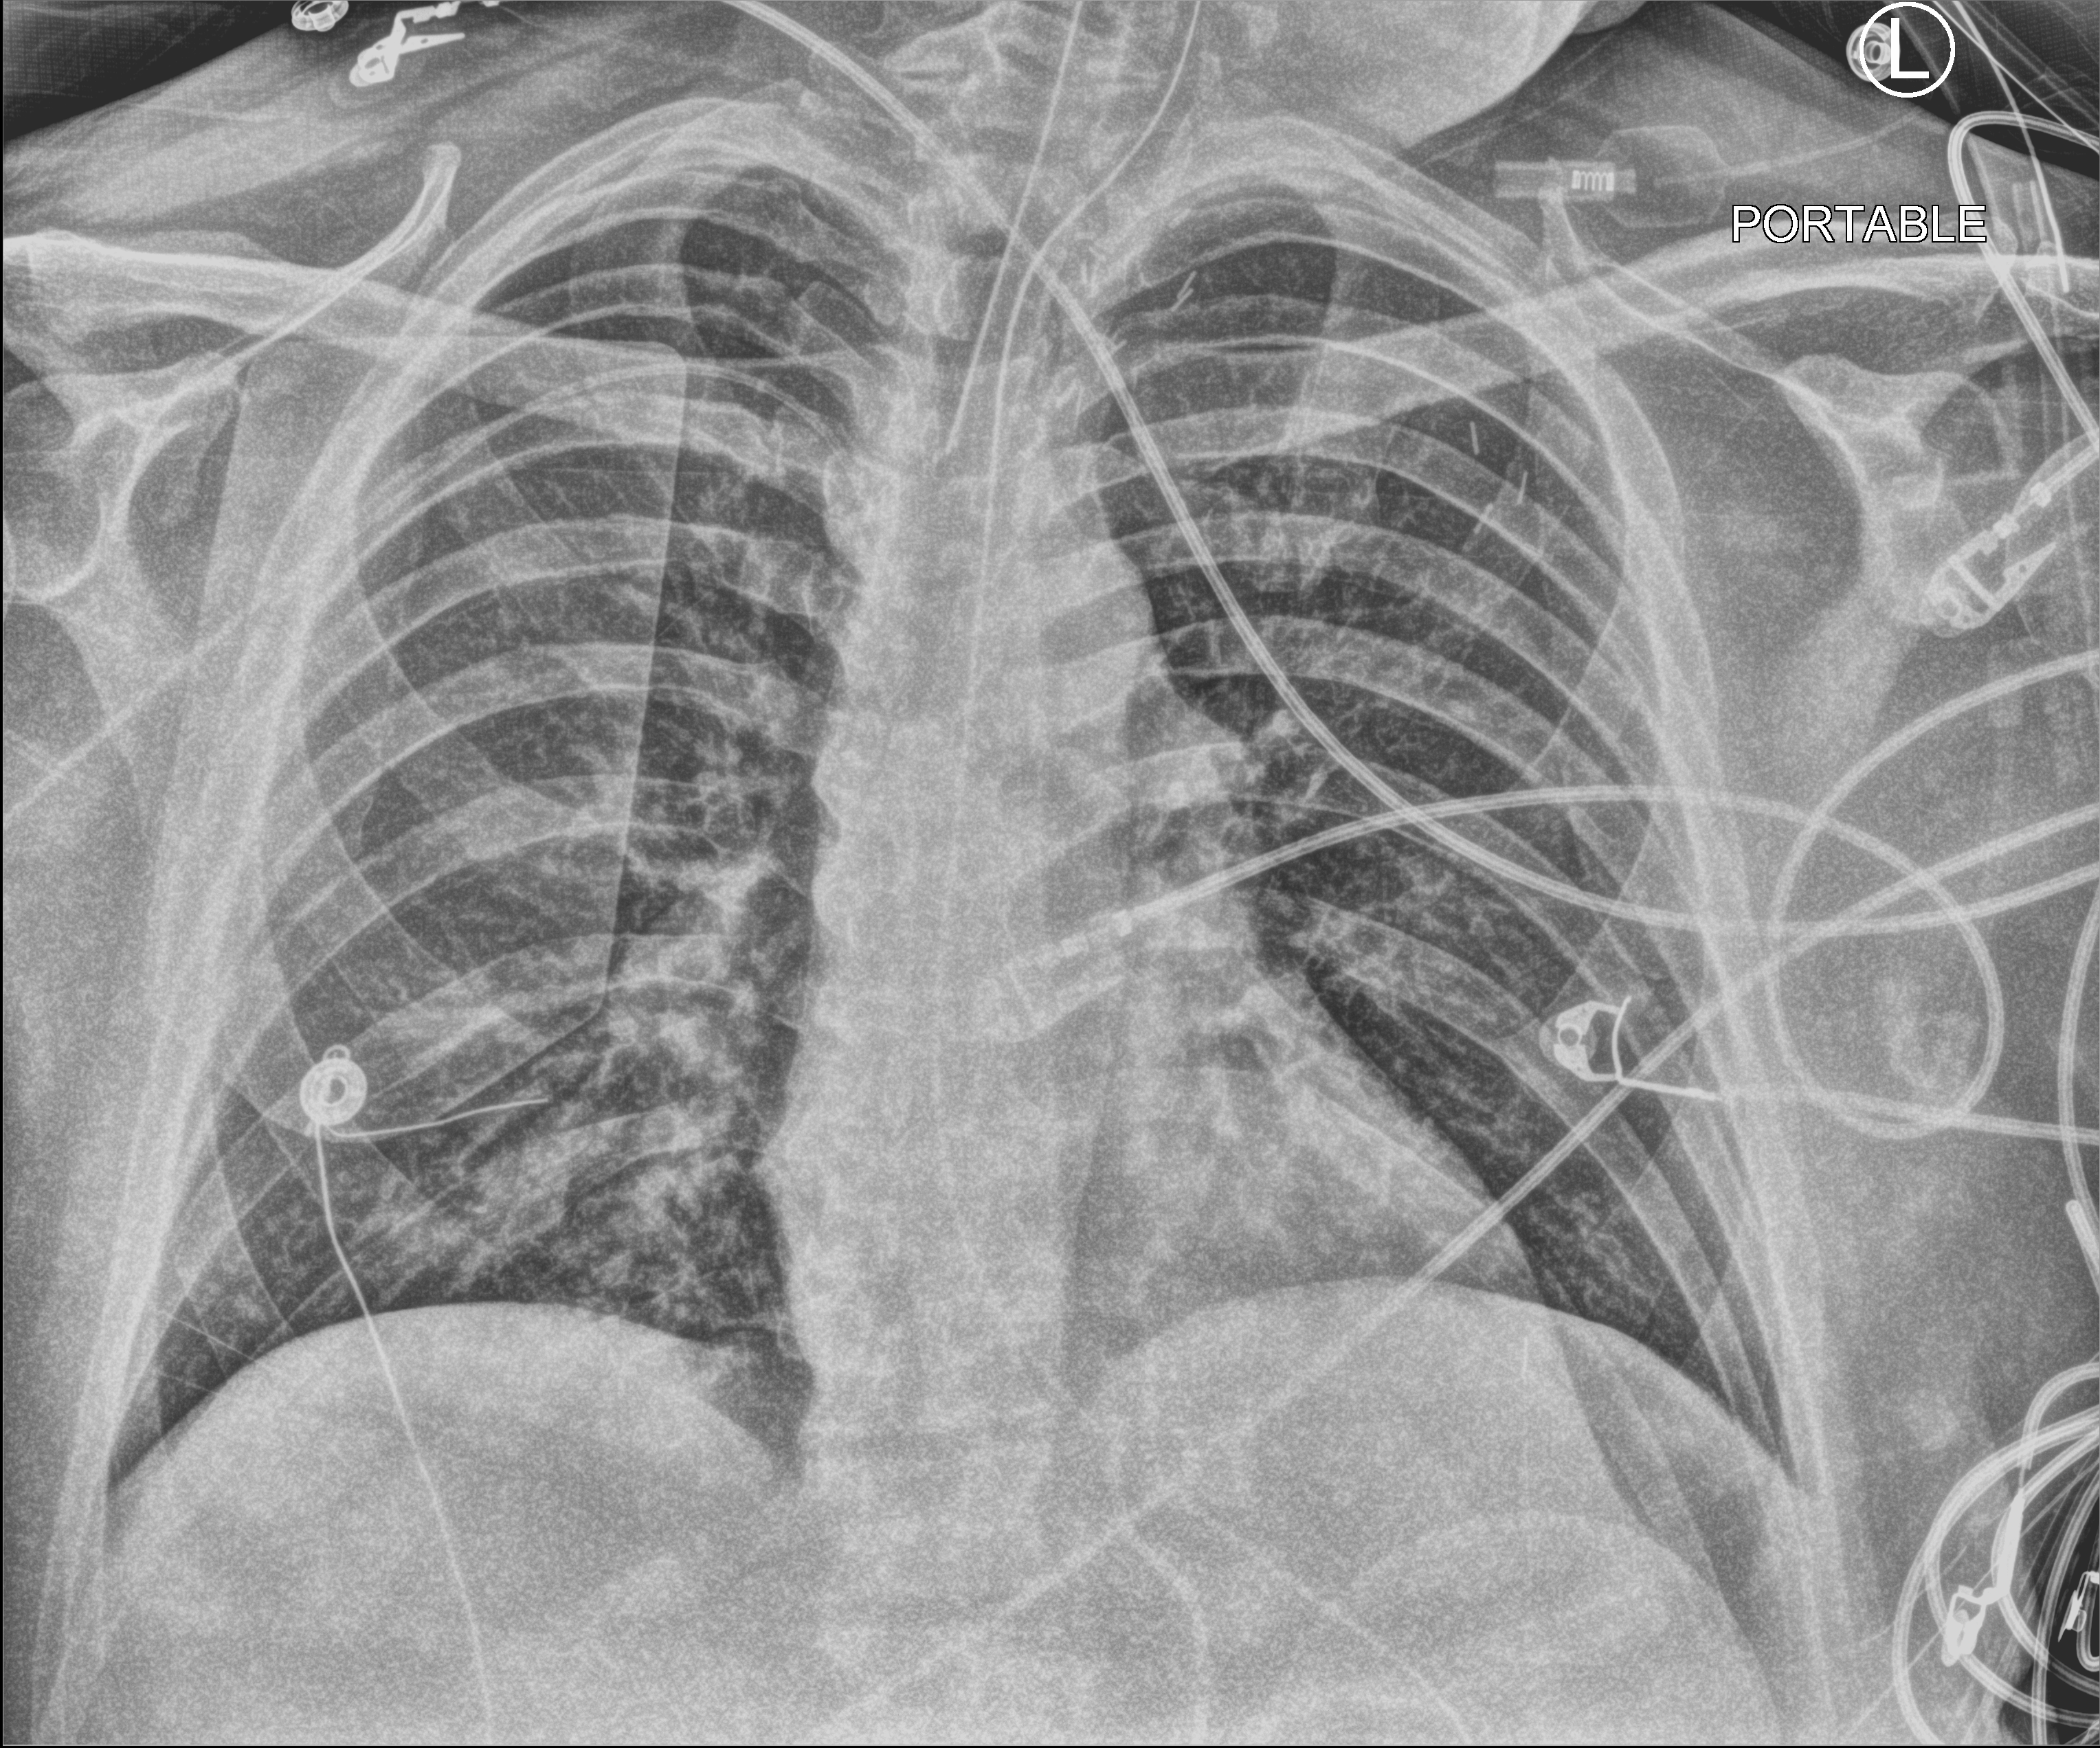
Portable chest radiograph. Adult patient hospitalised with COVID-19, age 18–59 years.
Hospital-stay facts (about this admission, not read from this image; timing relative to this image not recorded):
- mechanically ventilated during this hospital stay: yes
- length of hospital stay: 19 days
- admitted to intensive care during this hospital stay: yes